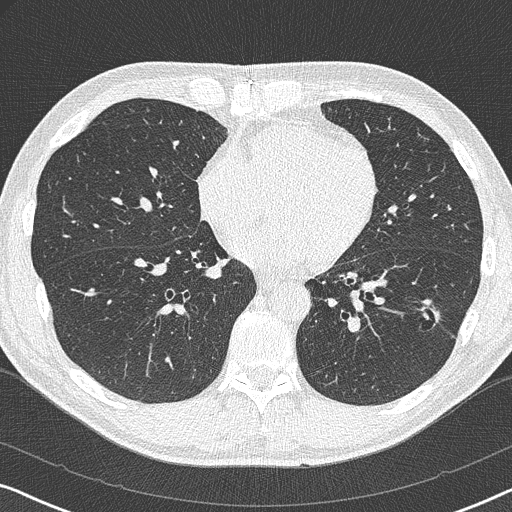
Axial slice from a low-dose chest CT screening exam. First (baseline) screen. Lung window (W 1500 / L -600 HU). 1 mm slice thickness. 512 × 512 image matrix, field of view 330 × 330 mm. Male participant, aged 59 years at enrolment.
Lesion marked by an expert reader, bounding box [x1, y1, x2, y2] px = [413, 302, 451, 340]. The screening reader recorded 2 non-calcified nodules or masses ≥4 mm on this exam (left lower lobe, right middle lobe); which of them this box marks is not recorded. Official screen result: positive, change unspecified: nodule(s) >= 4 mm or enlarging nodule(s), mass(es), or other non-specific abnormalities suspicious for lung cancer. Lung cancer was diagnosed 821 days after this screen: adenocarcinoma, NOS, left lower lobe, poorly differentiated (G3), stage IA (AJCC 6th edition), 20 mm at pathology.